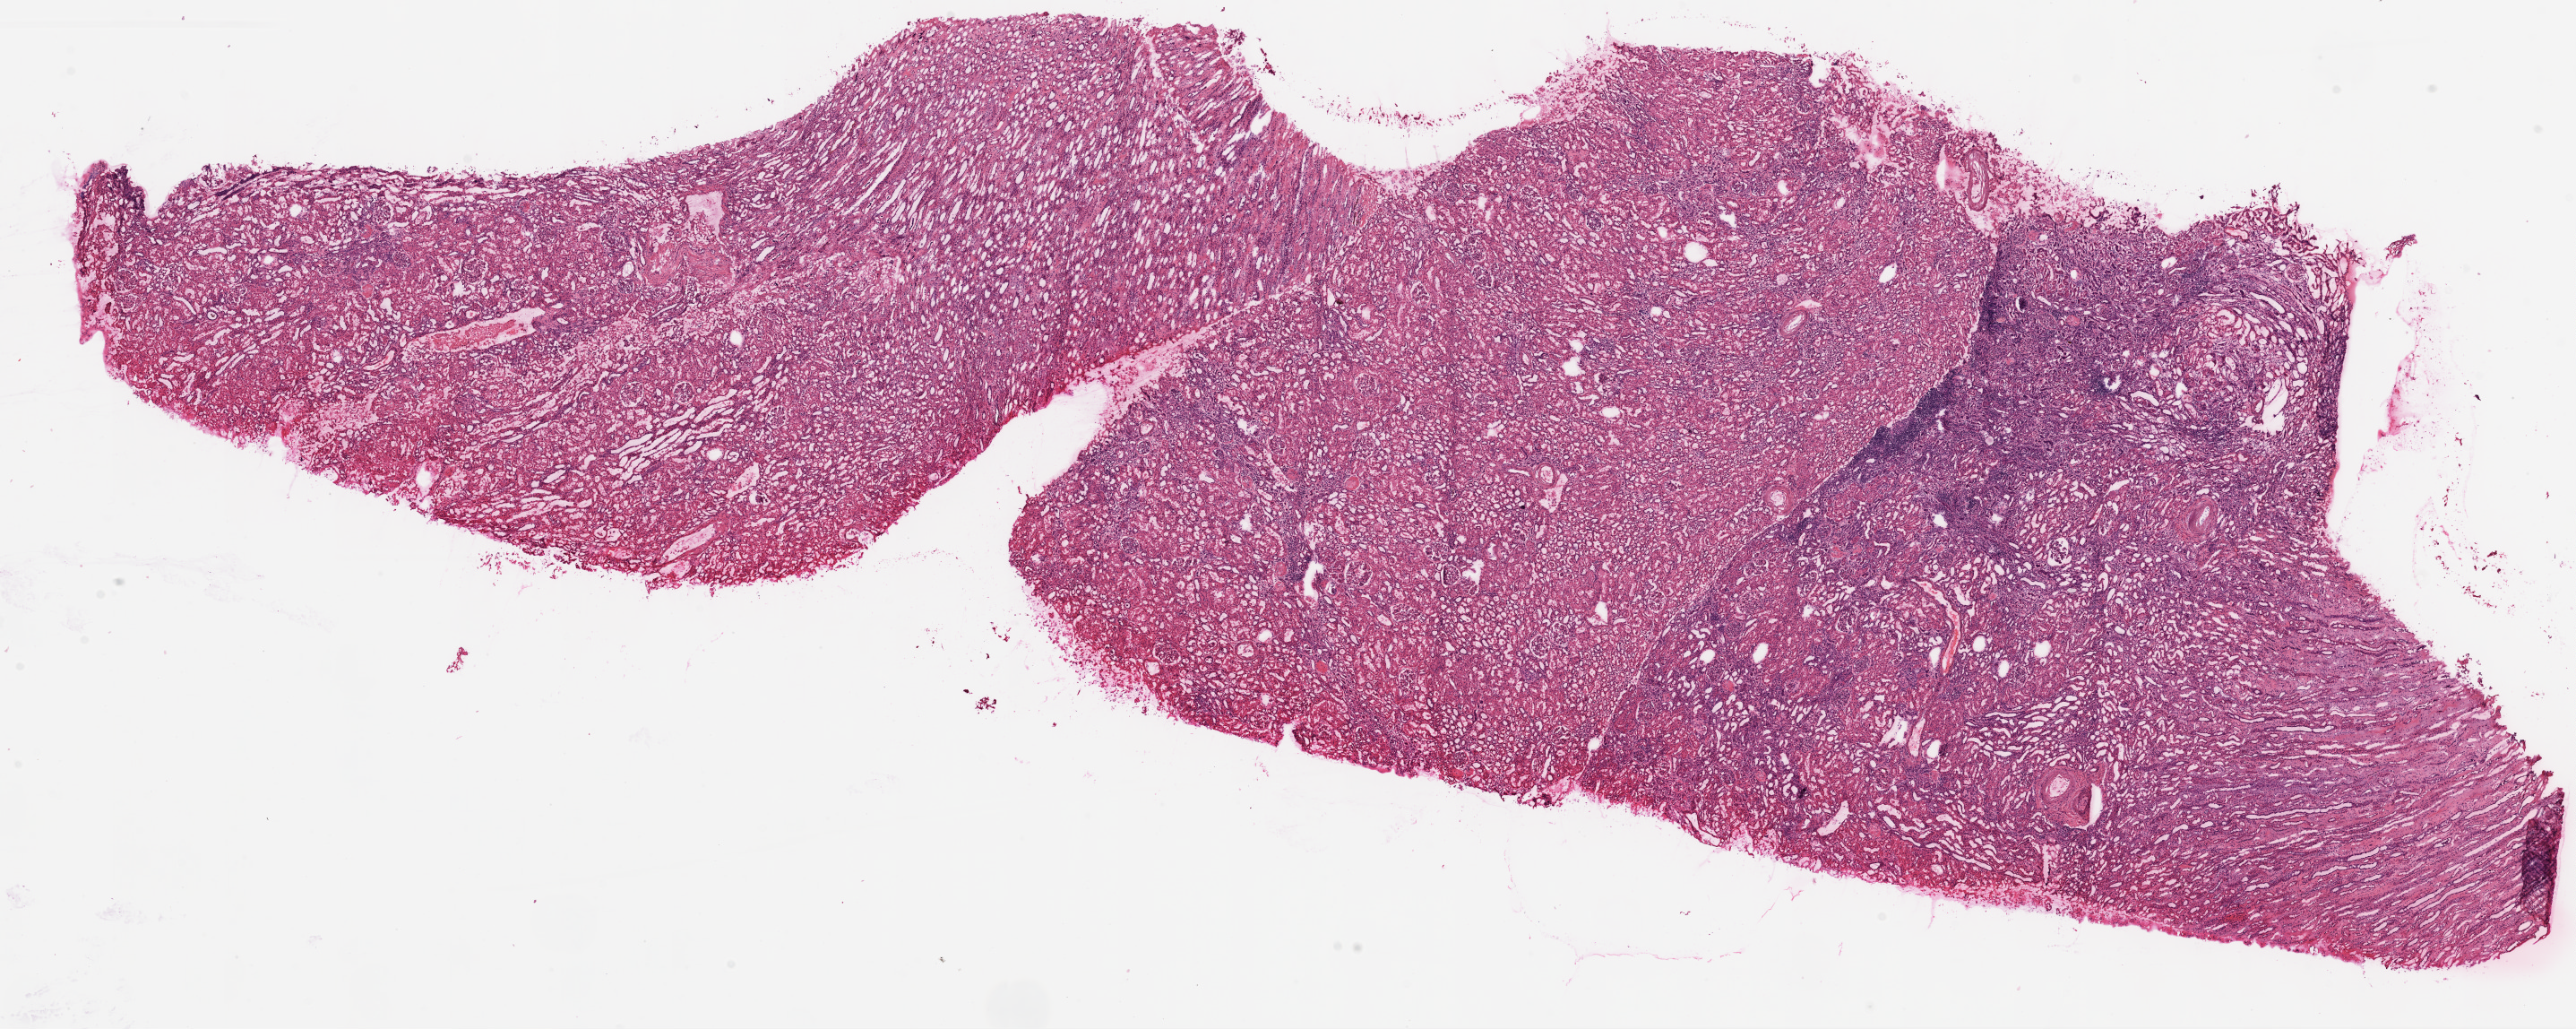
Whole-slide histology image, H&E, whole scanned area (about 23.1 x 9.2 mm) shown as a low-resolution overview, frozen section from the top of the tissue portion, kidney, solid tissue normal (non-tumour tissue) sample. Patient sex: female.
This section: solid tissue normal (non-tumour) sample from the same patient. Patient diagnosis: Clear cell adenocarcinoma, NOS.